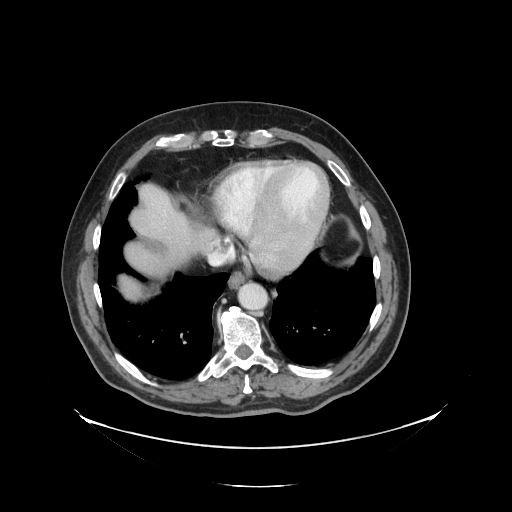
Contrast-enhanced abdominal CT, one axial slice. Position 121 of 138 along the scan axis. 120 kVp. Intravenous contrast given. Soft-tissue window (W 400 / L 40 HU). 512 × 512 image matrix. Male patient, age 77 years. Case-level facts recorded for this patient, not image findings: diagnosis: colorectal cancer liver metastases, imaged before liver resection; multiple liver metastases: no; largest metastasis: 1.5 cm; disease in both lobes: no.
Annotated regions visible in this slice (manually delineated by an expert):
- liver: bounding box (x1, y1, x2, y2) in pixels: (120, 186, 213, 299)
- planned liver remnant (the part of the liver to remain after resection): (120, 186, 213, 287)